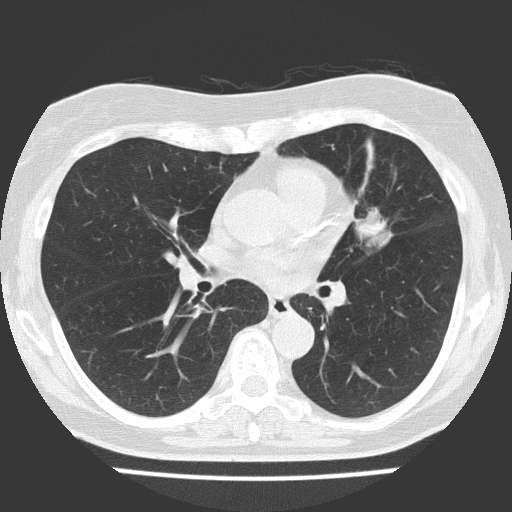
Low-dose screening chest CT, one axial slice; position 78 of 151 along the scan axis; reconstruction kernel FC51; 120 kVp; lung window (W 1500 / L -600 HU); 512 × 512 image matrix, field of view 309 × 309 mm.
Annotated regions visible in this slice (expert manual segmentation):
- lesion 1 (tumor, upper lobe of left lung): bounding box [x1, y1, x2, y2] px = [355, 209, 387, 237]